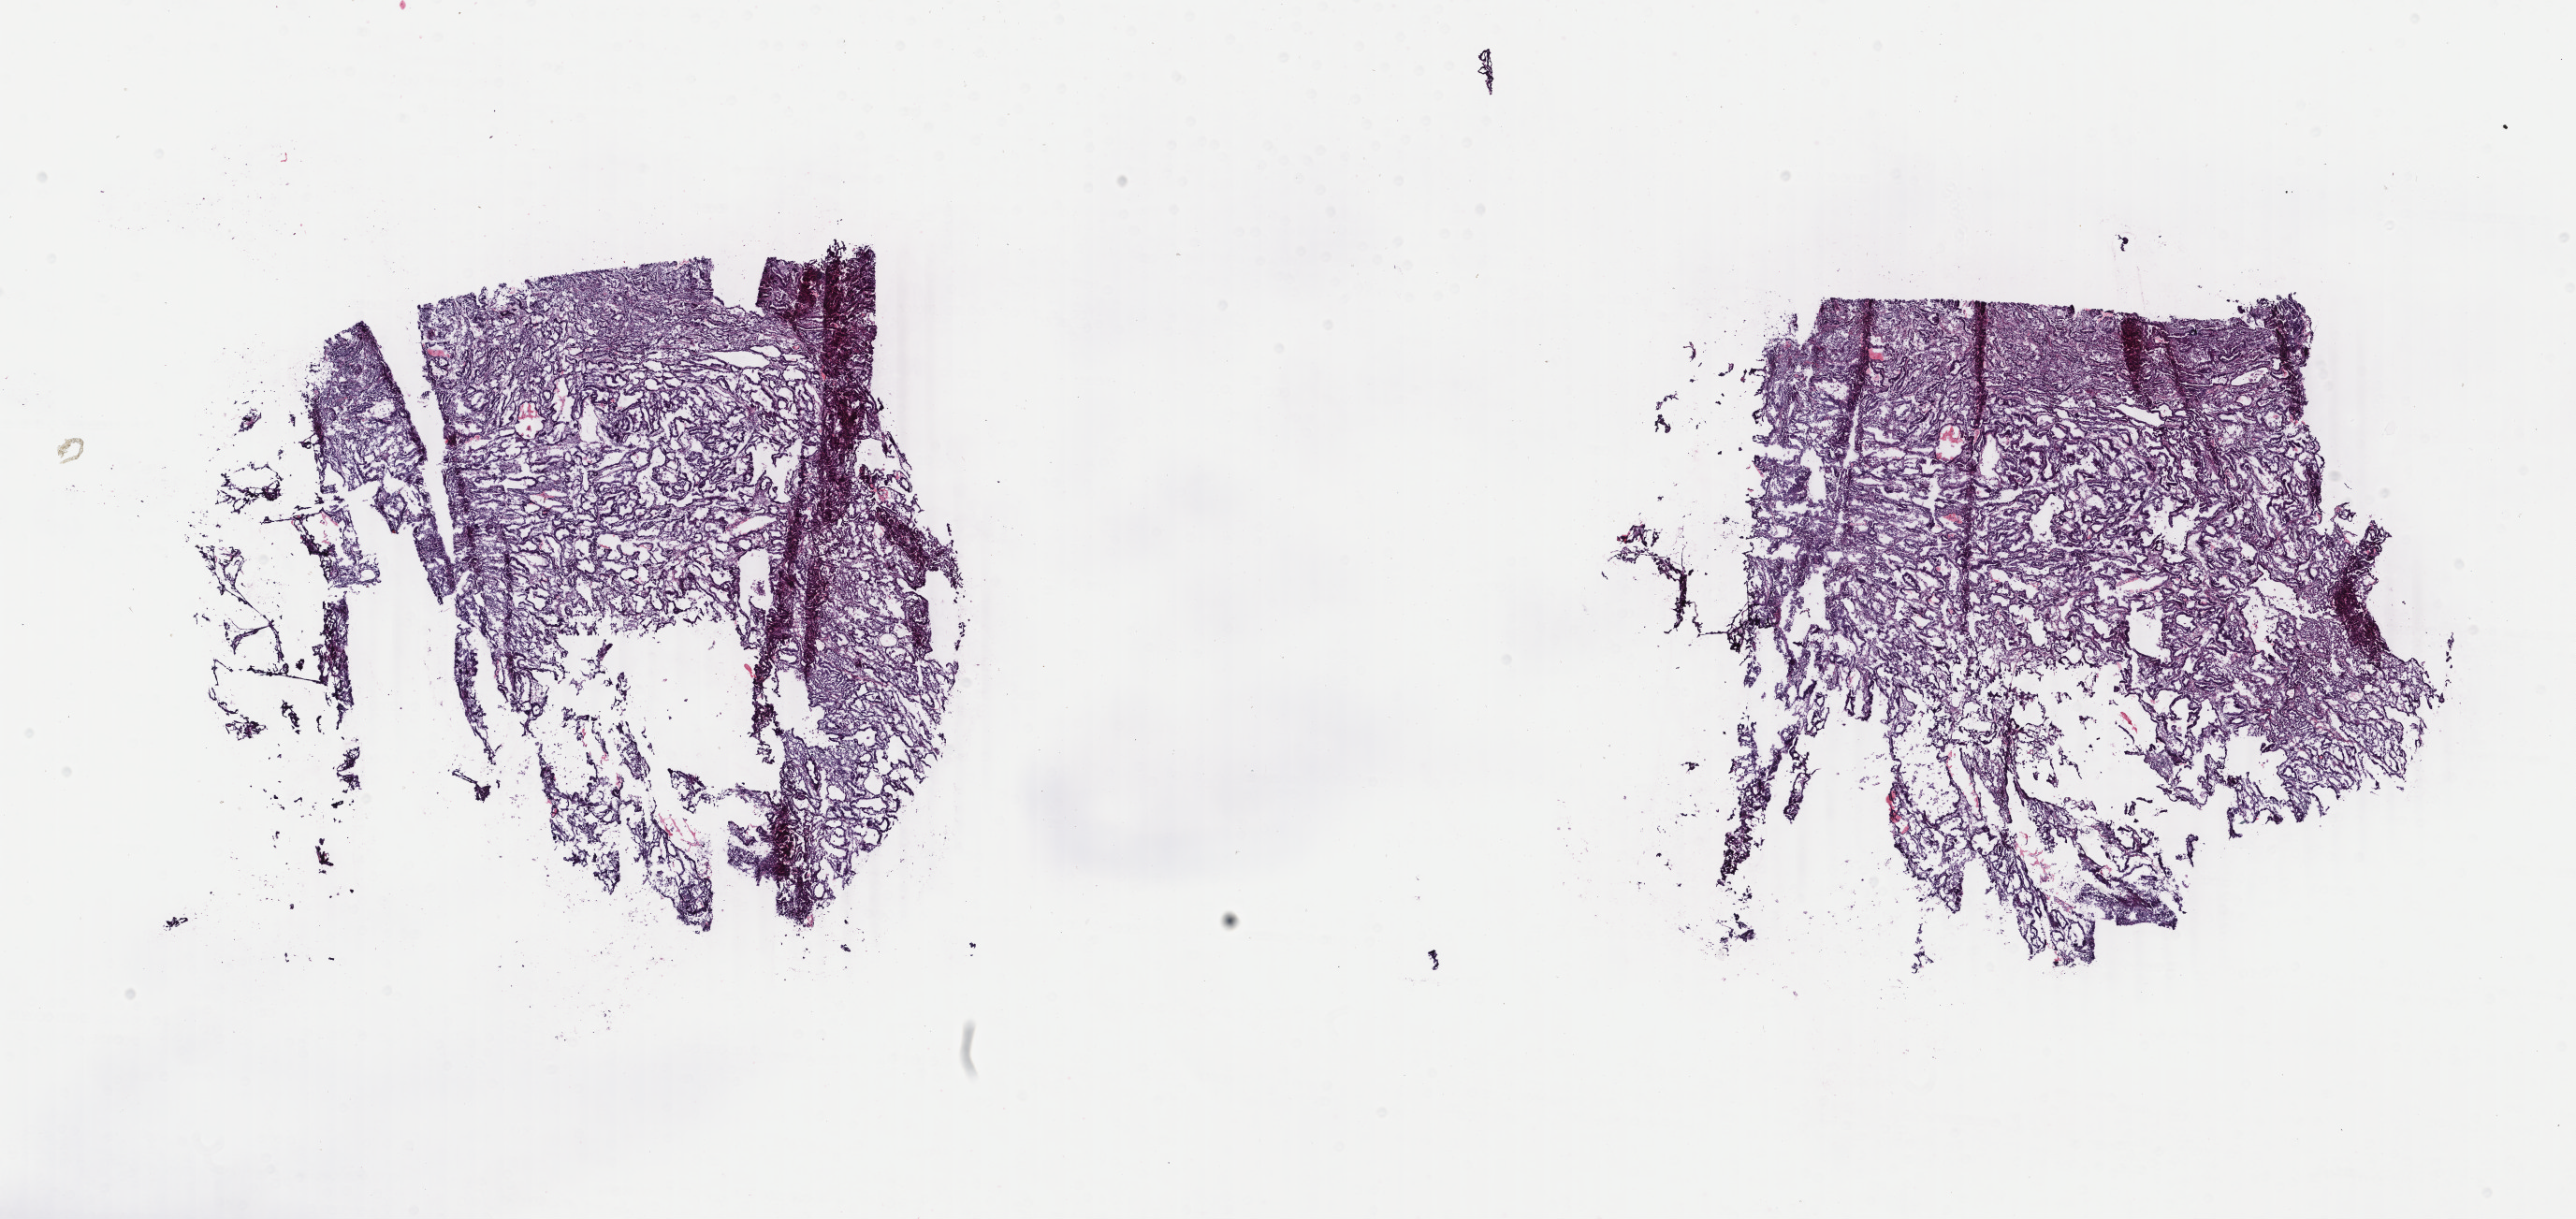
Whole-slide histology image, H&E-stained, whole scanned area (about 21.9 x 10.4 mm, acquisition: 40x scan) shown as a low-resolution overview, frozen section, uterus, primary tumour sample. Female patient; age at initial diagnosis 76 years. Histologic grade: G1 (well differentiated). Pathologist review of this section (percent, as recorded): tumour cells 100%, tumour nuclei 80%, normal cells 0%, stromal cells 0%, necrosis 0%. Infiltration values recorded for this section: lymphocyte infiltration 0%, monocyte infiltration 0%, neutrophil infiltration 0%.
Pathologic diagnosis: Endometrioid adenocarcinoma, NOS. FIGO stage: IA. Lymph nodes positive (case pathology): 0 of 10 examined.